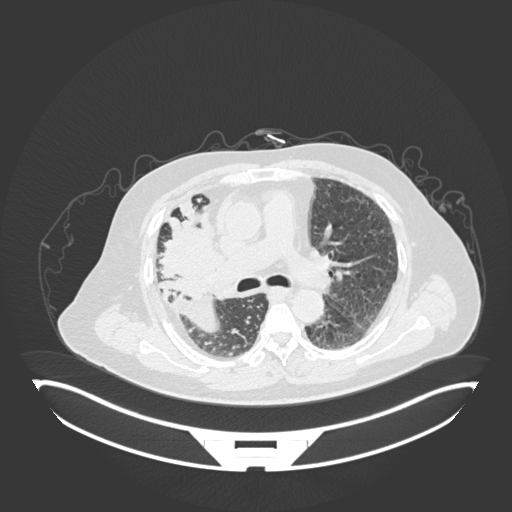
Chest CT, one axial slice. Lung window (W 1500 / L -600 HU). 512 × 512 image matrix. Patient: male, 69 years. Case-level facts recorded for this patient, not image findings: clinical TNM (as recorded): T4 N3 M1.
Annotated regions visible in this slice (bounding box drawn by a radiologist):
- lung tumour (recorded histology: adenocarcinoma): box from (x=165, y=210) to (x=228, y=295) px